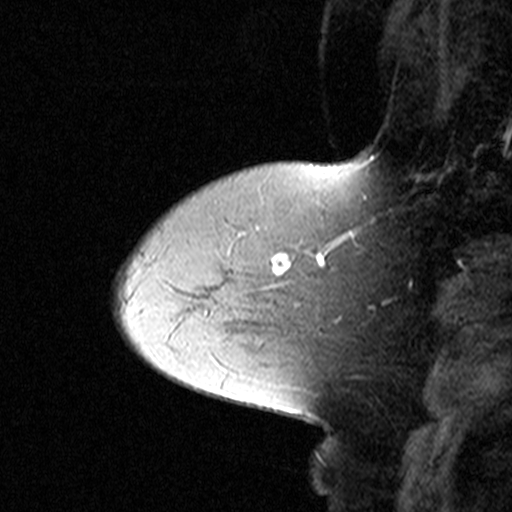
Breast MRI (dynamic contrast-enhanced), one sagittal slice; slice 11 of 44 in the series (ordered by position); dynamic contrast-enhanced study with each time point stored as its own series, time point 2 of 3 at this slice position (early post-contrast, ordered by acquisition time); 1.5 T; TE 4.5 ms, TR 11 ms; 3 mm slice thickness; 512 × 512 image matrix, field of view 200 × 200 mm. Patient: female, 50 years. Case-level facts recorded for this patient, not image findings: setting: breast cancer imaged before/during neoadjuvant chemotherapy; receptor status: HR-positive, HER2-negative.
Structures marked on this image (semi-automatic segmentation, software-assisted and operator-edited):
- analysis volume of interest (the breast-tissue region the enhancement analysis was run in; not a lesion): box from (x=180, y=198) to (x=302, y=311) px
- tumour enhancement mask (voxels above the 90 % enhancement threshold inside the analysis volume of interest): (x=273, y=253)–(x=290, y=272)